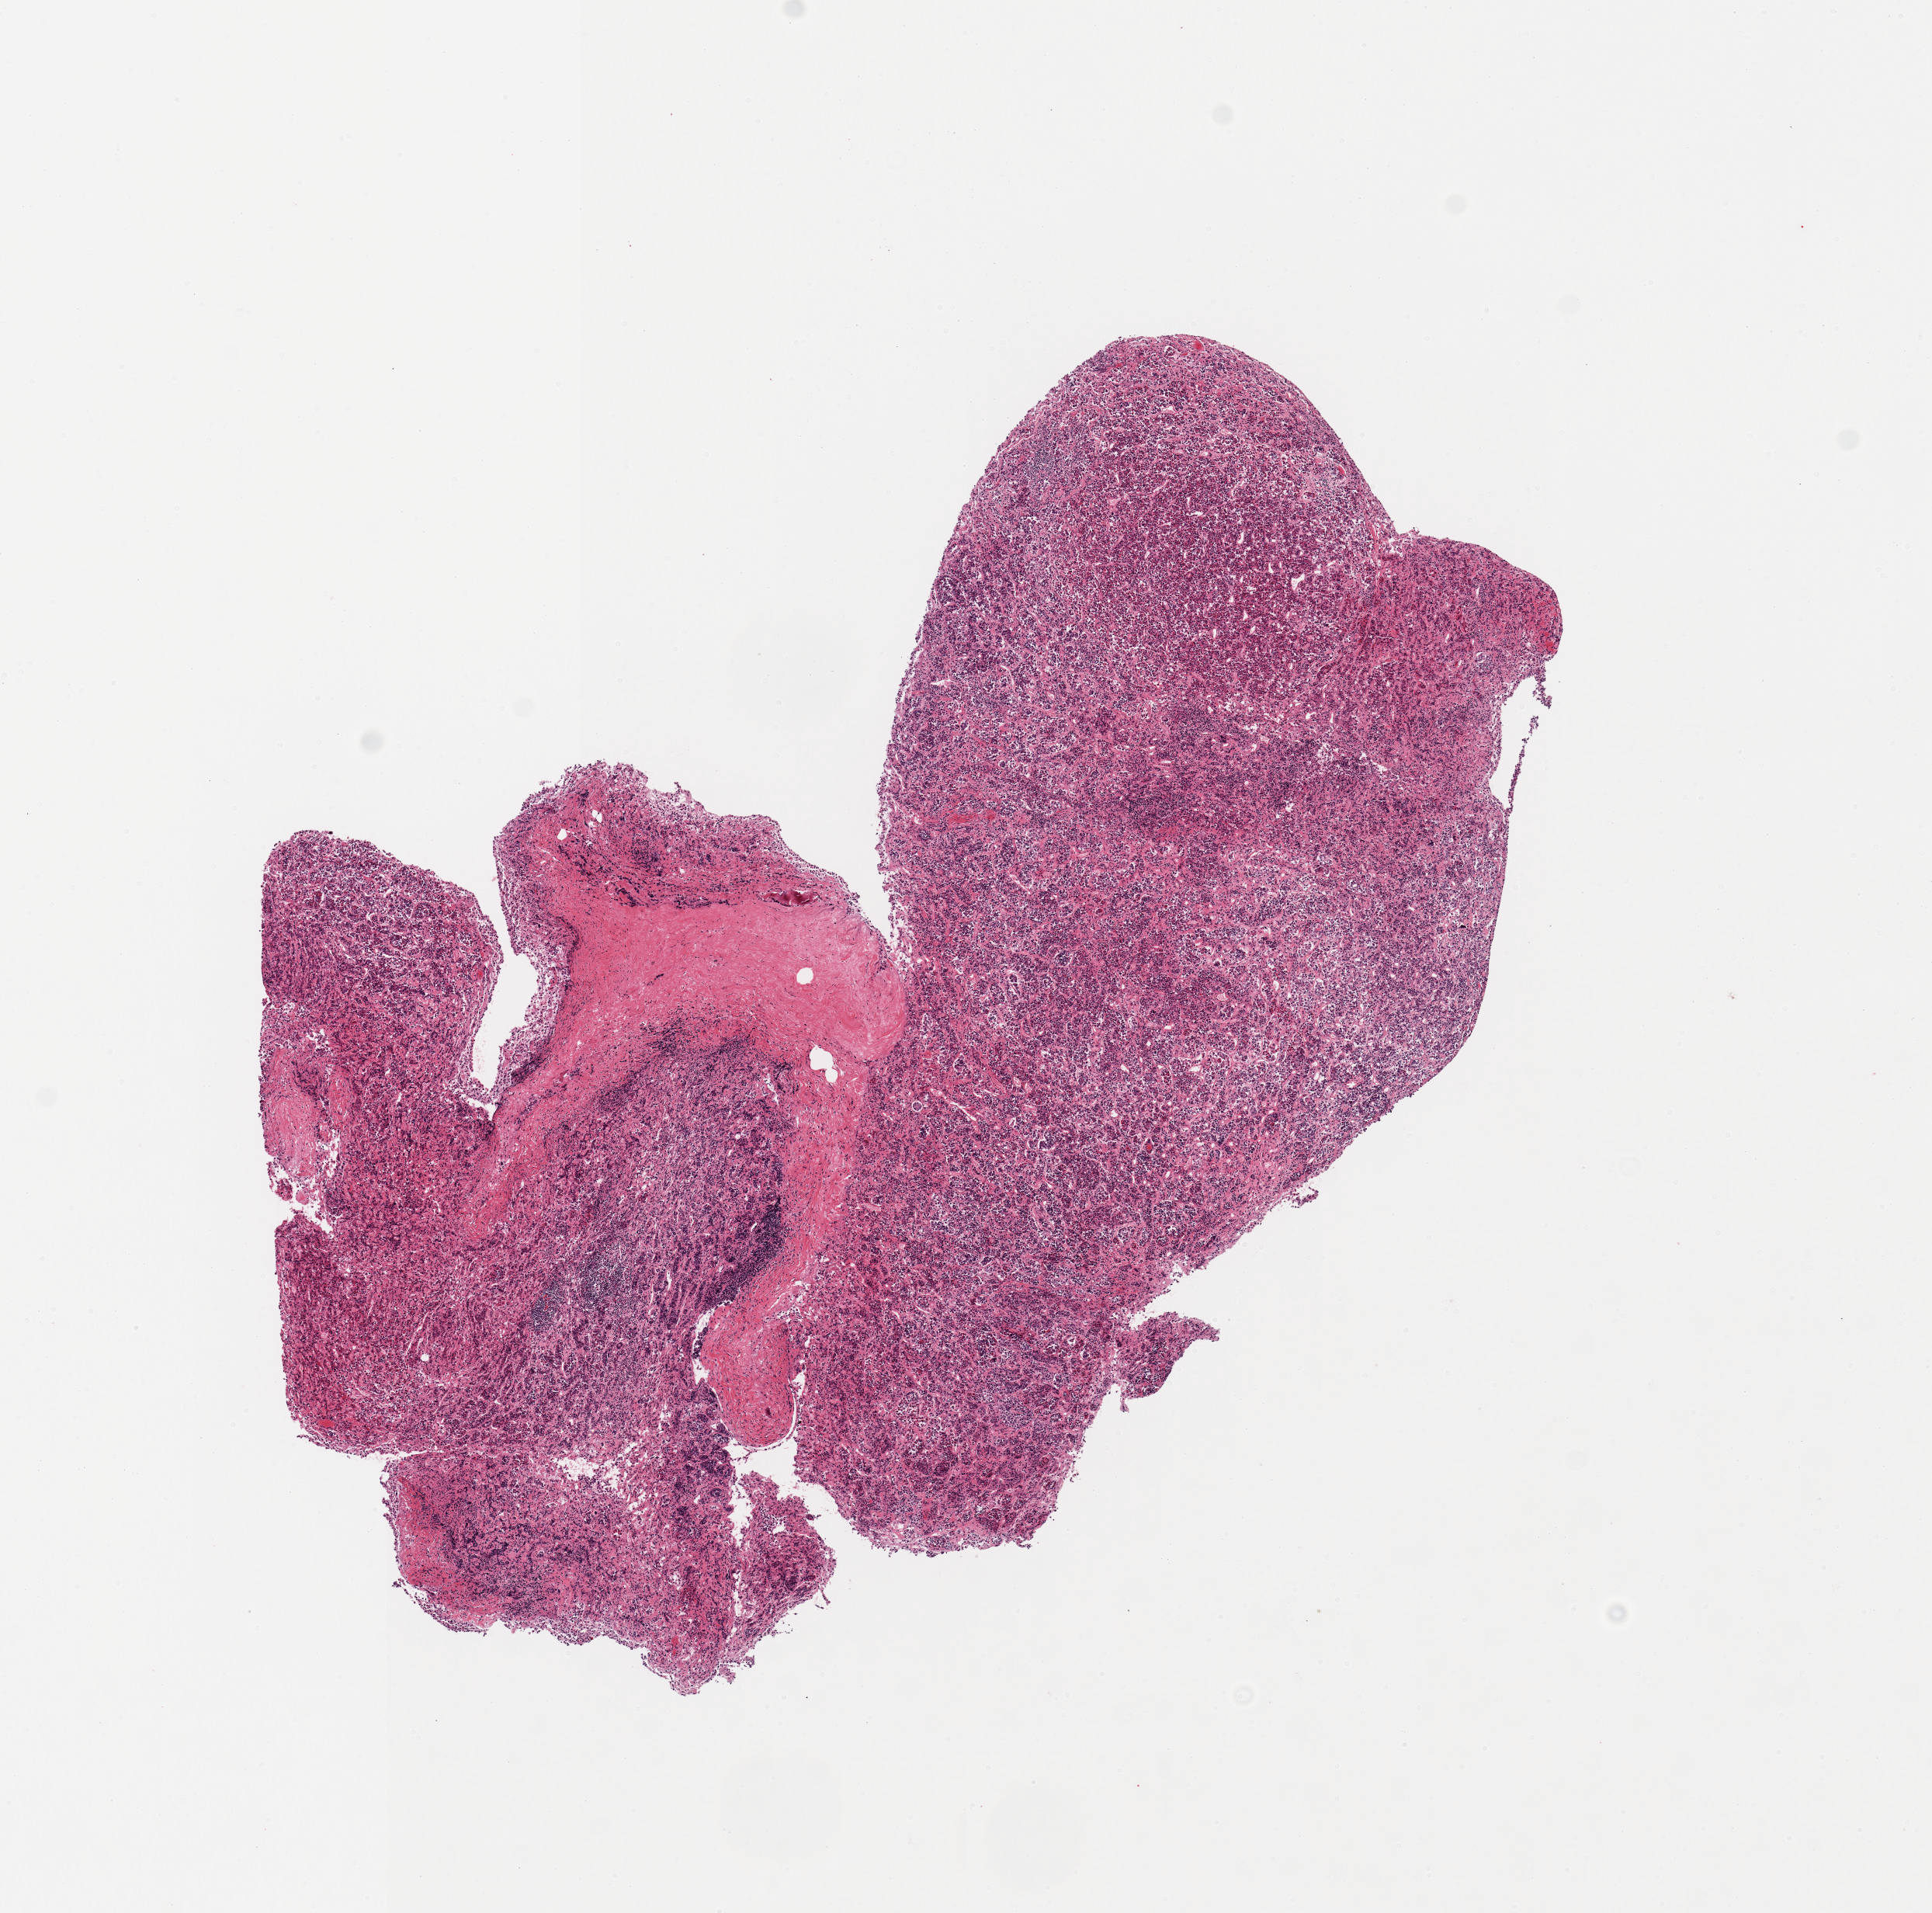
Hematoxylin and eosin (H&E) whole-slide image — a low-resolution overview of the entire scanned area, about 9.8 x 9.7 mm; PAXgene-fixed, paraffin-embedded tissue; target tissue: pituitary; donor tissue sample. Female donor.
Pathologist's review note for this sample: 2 pieces, adenohypophysis, ~15% dura.